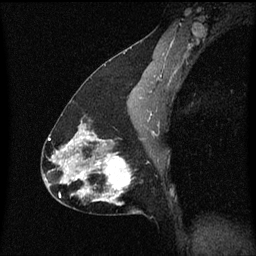
Breast MRI (dynamic contrast-enhanced), one sagittal slice. Position 33 of 60 along the scan axis. Dynamic contrast-enhanced series, image 2 of 3 at this slice position (ordered by acquisition). 1.5 T. TE 4.2 ms, TR 8.4 ms. 2 mm slice thickness. 256 × 256 image matrix. Female patient, age 47 years.
Annotated regions visible in this slice (semi-automatically segmented with operator editing):
- analysis volume of interest (the breast-tissue region the enhancement analysis was run in; not a lesion): box from (x=81, y=138) to (x=143, y=215) px
- tumour enhancement mask (voxels above the 70 % enhancement threshold inside the analysis volume of interest): (x=81, y=138)–(x=131, y=203)